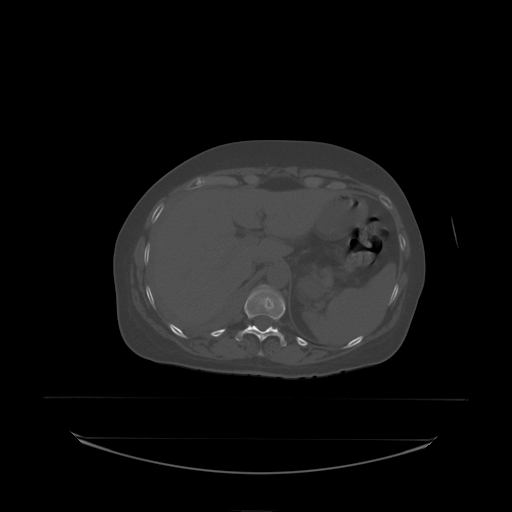
CT including the spine, one axial slice. Slice 103 of 242 in the series (ordered by position). Bone window (W 1800 / L 400 HU). 512 × 512 image matrix, field of view 500 × 500 mm. Patient: female, 53 years. From the clinical record (not read from this slice): primary cancer: lung.
Structures marked on this image (semi-automatic segmentation, software-assisted and operator-edited):
- T11 vertebra: bounding box <237,290,286,338> (left, top, right, bottom; pixels)
- T12 vertebra: <256,285,275,292>